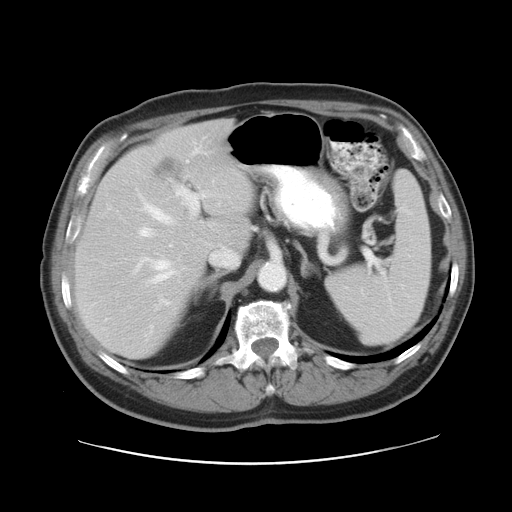
Contrast-enhanced abdominal CT, one axial slice. Slice 19 of 28 in the series (ordered by position). 120 kVp. Intravenous contrast given. Soft-tissue window (W 400 / L 40 HU). 7.5 mm slice thickness. 512 × 512 image matrix, field of view 402 × 402 mm. Male patient, age 74 years. From the clinical record (not read from this slice): diagnosis: colorectal cancer liver metastases, imaged before liver resection; multiple liver metastases: no; largest metastasis: 5 cm; disease in both lobes: no.
Annotated regions visible in this slice (manually delineated by an expert):
- hepatic veins: bounding box (x1, y1, x2, y2) in pixels: (133, 202, 220, 283)
- liver: (76, 121, 252, 357)
- planned liver remnant (the part of the liver to remain after resection): (76, 174, 210, 357)
- portal vein (with intrahepatic branches): (140, 148, 209, 247)
- liver metastasis: (153, 157, 183, 178)